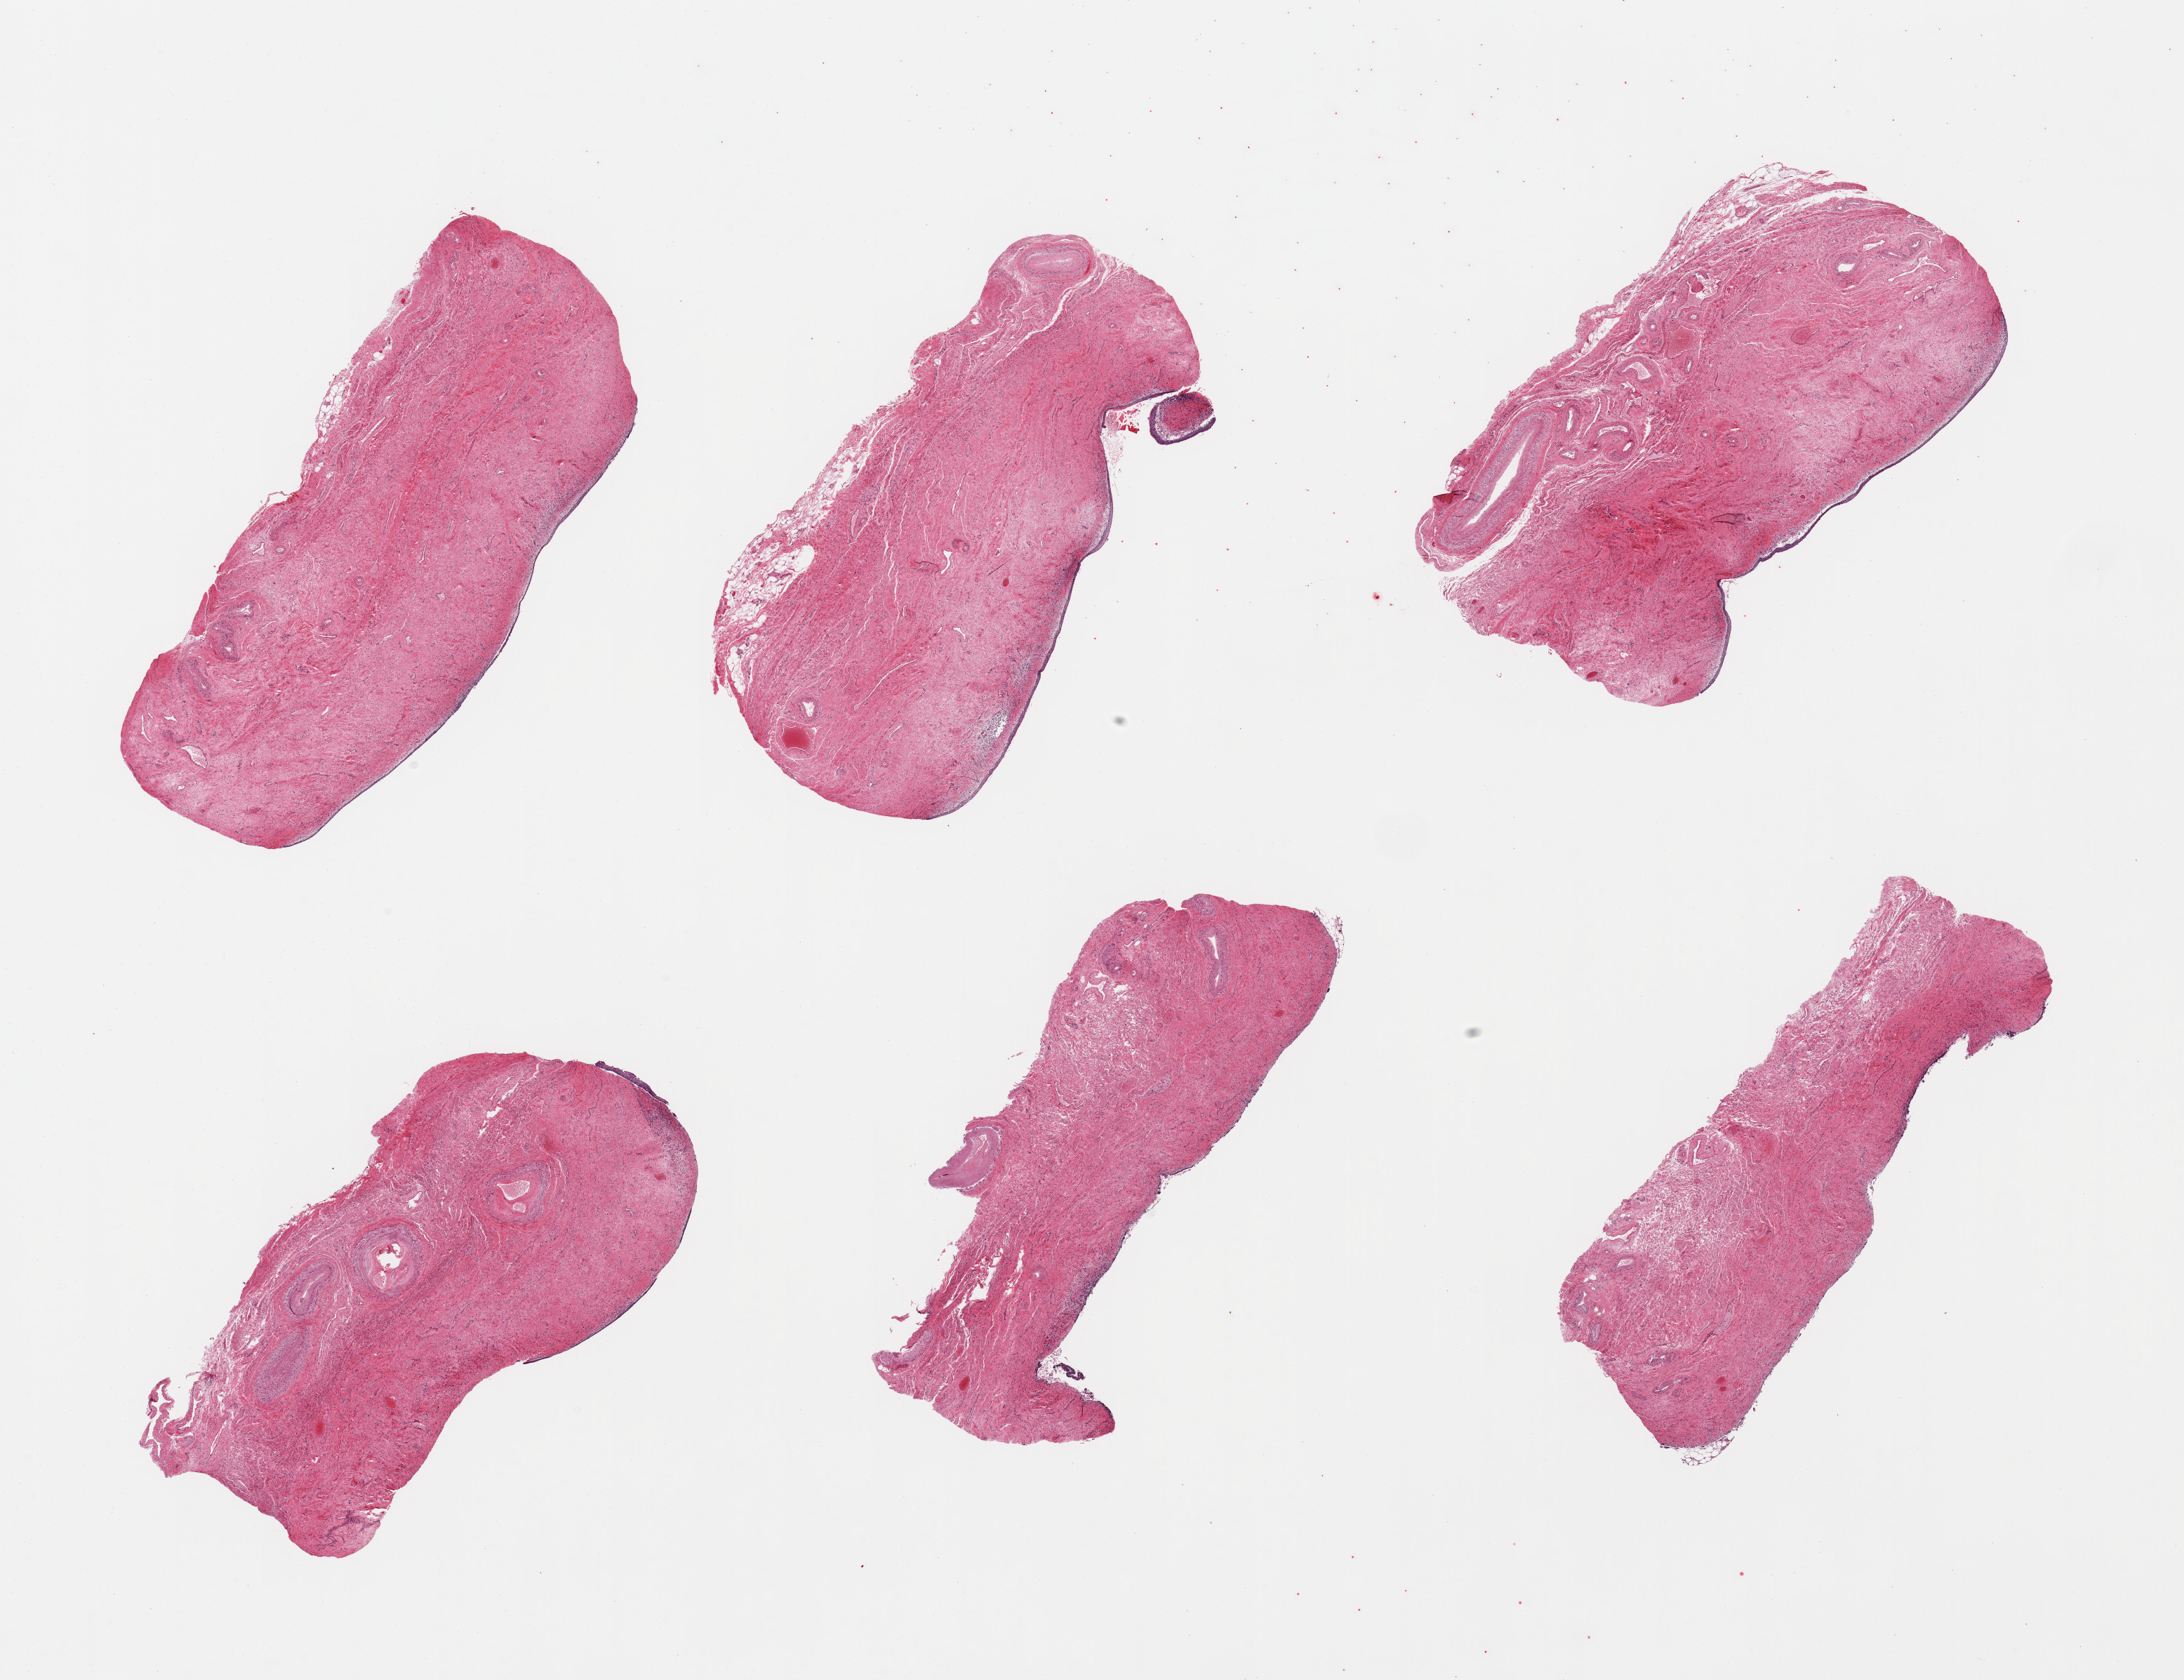
H&E whole-slide image, brightfield — shown as a low-resolution overview of the whole scanned area (about 24.6 x 18.9 mm, from a 20x scan), PAXgene-fixed, paraffin-embedded tissue, section of vagina (target tissue), tissue donor sample. Donor: female.
Pathologist's review note for this sample: 6 pieces; atrophic and partially sloughed epithelium.